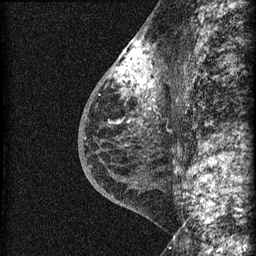
Breast MRI (dynamic contrast-enhanced), one sagittal slice. Slice 31 of 60 in the series (ordered by position). Dynamic contrast-enhanced series, image 2 of 3 at this slice position (ordered by acquisition). 1.5 T. TE 4.2 ms, TR 22.7 ms. 1.5 mm slice thickness. 256 × 256 image matrix, field of view 180 × 180 mm. Patient: female, 48 years. Case-level facts recorded for this patient, not image findings: setting: breast cancer imaged before/during neoadjuvant chemotherapy; receptor status: triple-negative.
Structures marked on this image (semi-automatically segmented with operator editing):
- analysis volume of interest (the breast-tissue region the enhancement analysis was run in; not a lesion): box from (x=115, y=34) to (x=169, y=162) px
- tumour enhancement mask (voxels above the 90 % enhancement threshold inside the analysis volume of interest): (x=115, y=39)–(x=155, y=94)